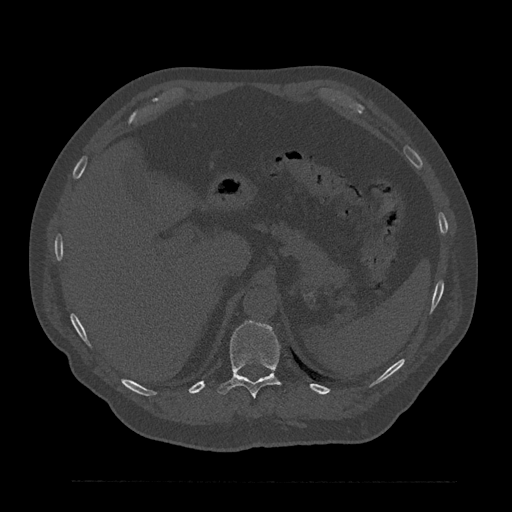
CT including the spine, one axial slice; bone window (W 1800 / L 400 HU); 0.5 mm slice thickness; 512 × 512 image matrix, field of view 430 × 430 mm. Male patient, age 61 years. From the clinical record (not read from this slice): primary cancer: prostate.
Outlined on this slice (semi-automatically segmented with operator editing):
- T11 vertebra: bounding box <217,321,282,398> (left, top, right, bottom; pixels)